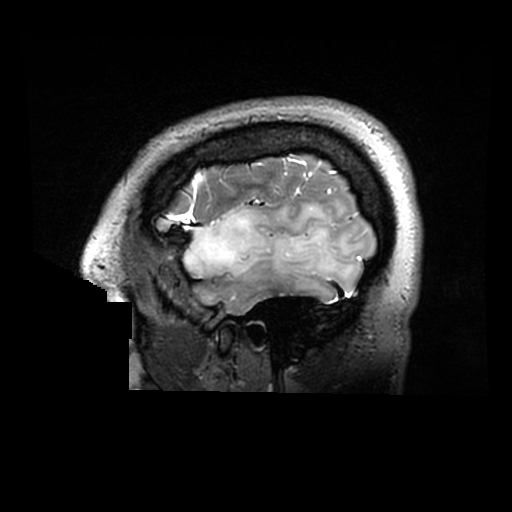
Brain MRI from a brain-tumour surgery series, one sagittal slice; slice 245 of 320 in the series (ordered by position); 0.6 mm slice thickness; 512 × 512 image matrix, field of view 240 × 240 mm. Case-level facts recorded for this patient, not image findings: histopathology: Astrocytoma; WHO grade: 2; IDH mutation: yes.
Annotated regions visible in this slice (outlined manually by an expert reader):
- tumour: bounding box (x1, y1, x2, y2) in pixels: (184, 201, 352, 297)